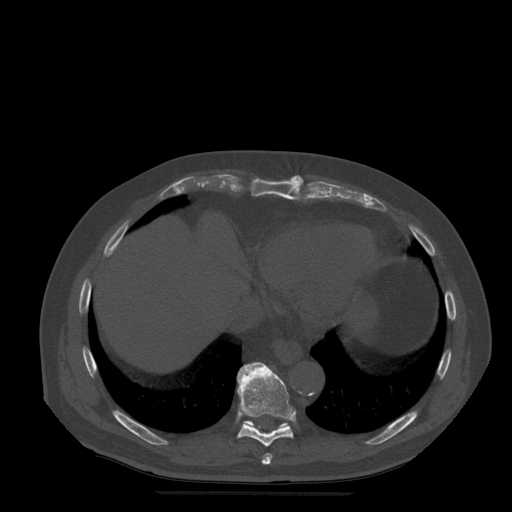
CT including the spine, one axial slice; position 286 of 522 along the scan axis; bone window (W 1800 / L 400 HU); 1.25 mm slice thickness; 512 × 512 image matrix, field of view 420 × 420 mm. Patient age 72 years. From the clinical record (not read from this slice): primary cancer: prostate.
Outlined on this slice (semi-automatic segmentation, software-assisted and operator-edited):
- T10 vertebra: box from (x=259, y=423) to (x=289, y=430) px
- T8 vertebra: (x=262, y=454)–(x=273, y=465)
- T9 vertebra: (x=237, y=363)–(x=294, y=447)